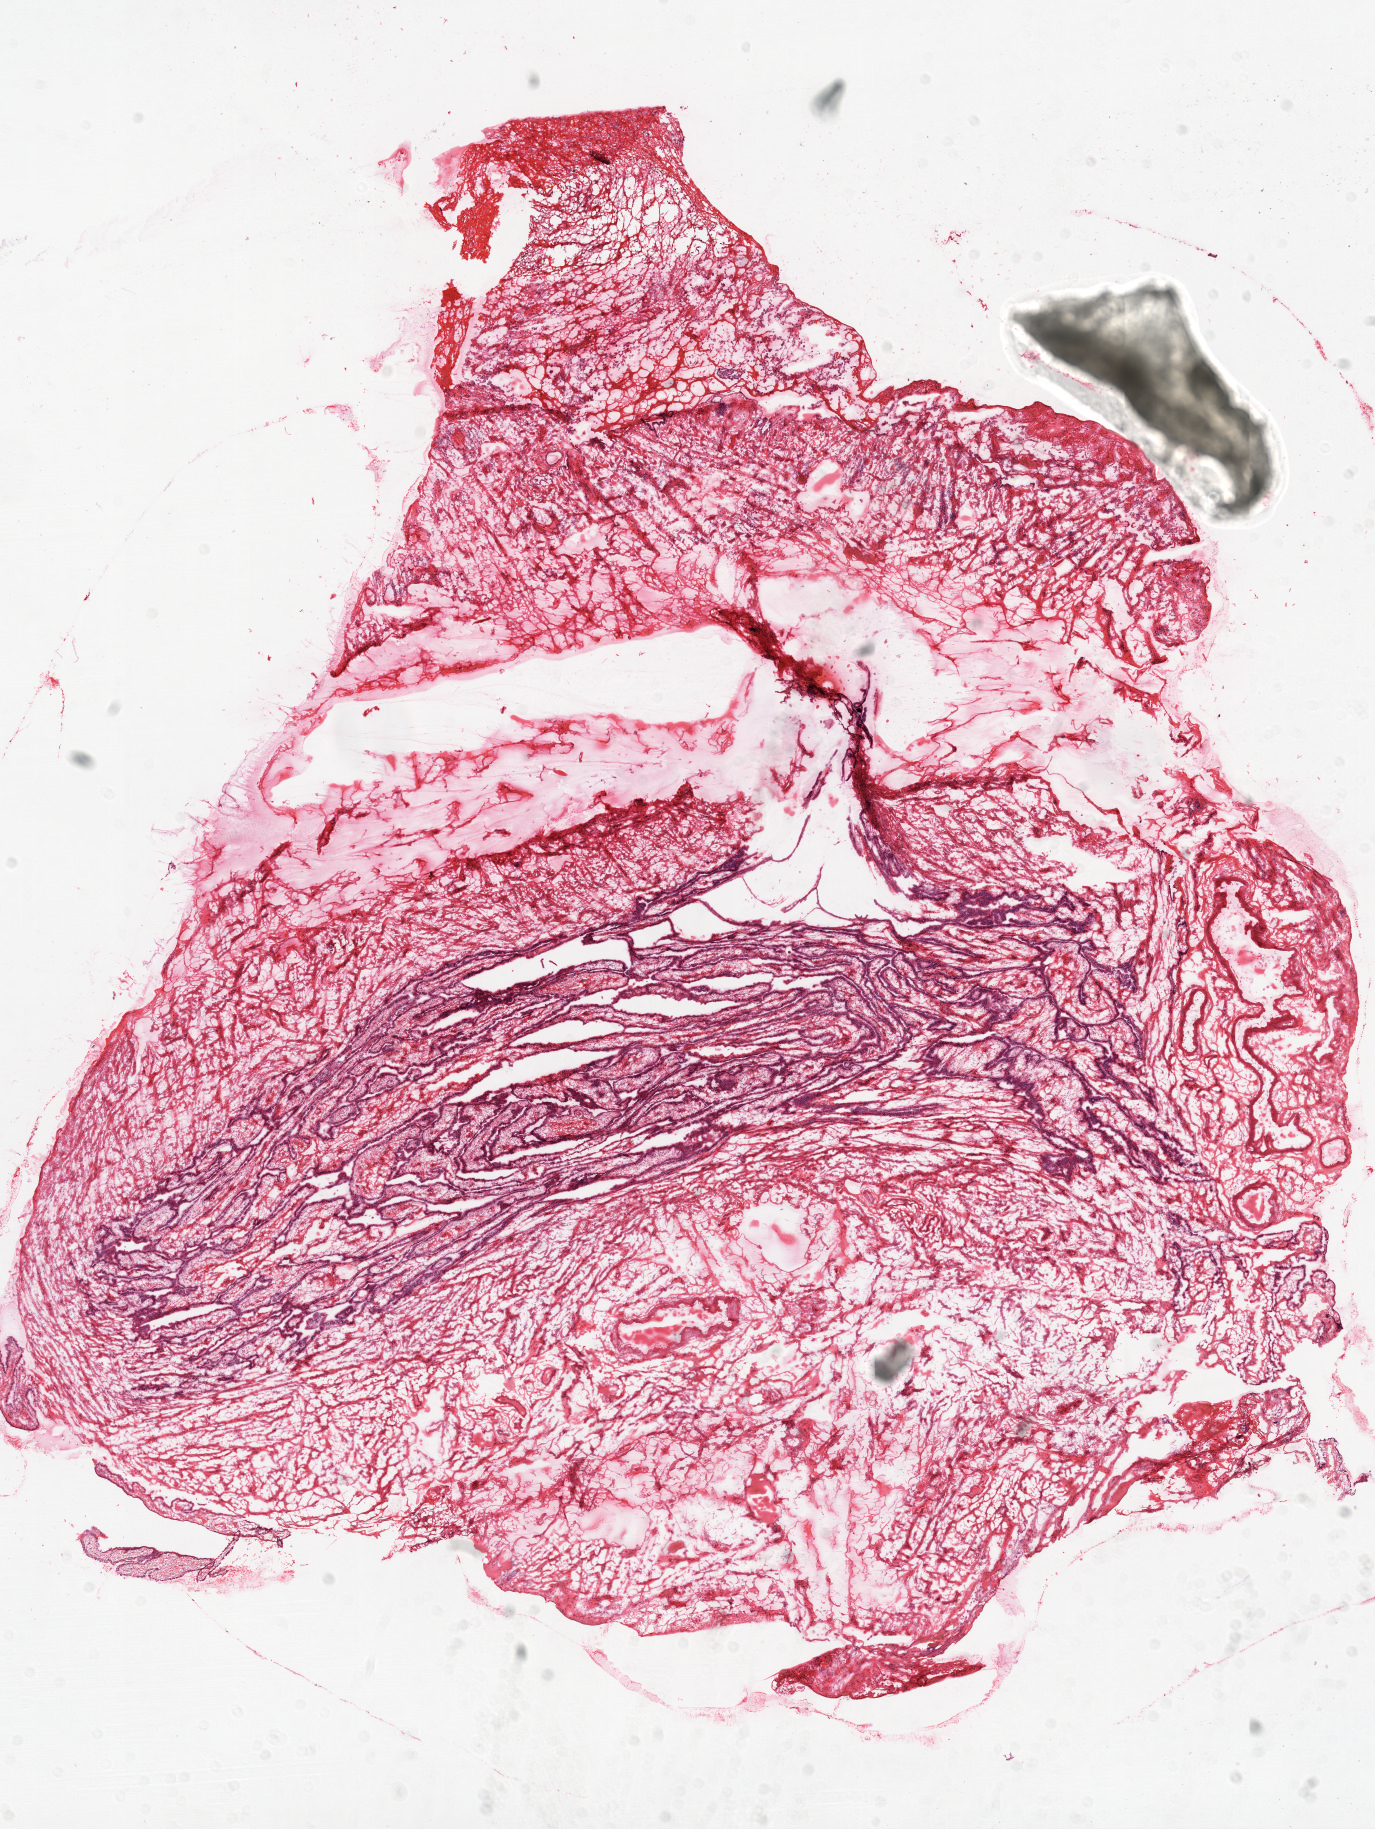
H&E whole-slide image, a low-resolution overview of the entire scanned area, about 11.0 x 14.7 mm (slide scanned at 20x); frozen section from the top of the tissue portion; sample: solid tissue normal (non-tumour tissue), ovary. Female patient; age at initial diagnosis 46 years.
This section: solid tissue normal sample (biorepository sample class). Patient diagnosis: Serous cystadenocarcinoma, NOS.